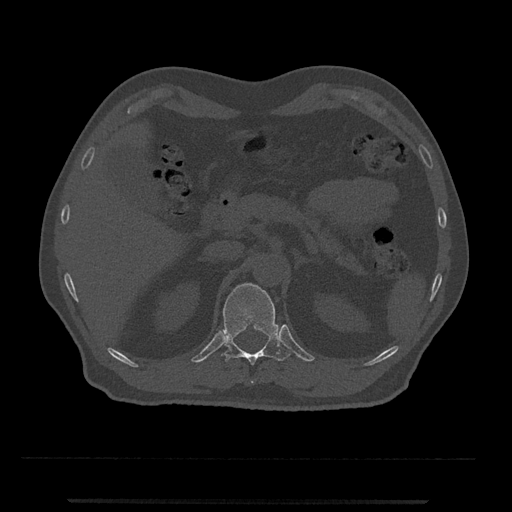
CT including the spine, one axial slice. Position 405 of 797 along the scan axis. Bone window (W 1800 / L 400 HU). 0.5 mm slice thickness. 512 × 512 image matrix. Patient: male, 63 years. From the clinical record (not read from this slice): primary cancer: prostate.
Annotated regions visible in this slice (semi-automatic segmentation, software-assisted and operator-edited):
- T12 vertebra: box from (x=220, y=283) to (x=290, y=383) px